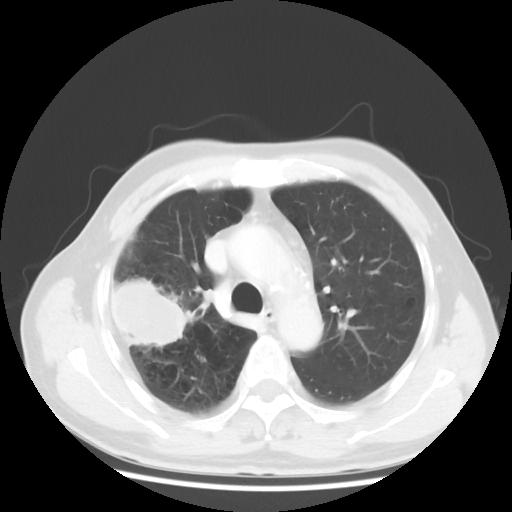
Chest CT, one axial slice. Position 35 of 50 along the scan axis. 120 kVp. Lung window (W 1500 / L -600 HU). 5 mm slice thickness. 512 × 512 image matrix. Patient: male, 69 years. Case-level facts recorded for this patient, not image findings: clinical TNM (as recorded): T3 N0 M0; histopathological grade: G3.
Annotated regions visible in this slice (bounding box drawn by a radiologist):
- lung tumour (recorded histology: adenocarcinoma): bounding box [x1, y1, x2, y2] px = [113, 270, 198, 353]